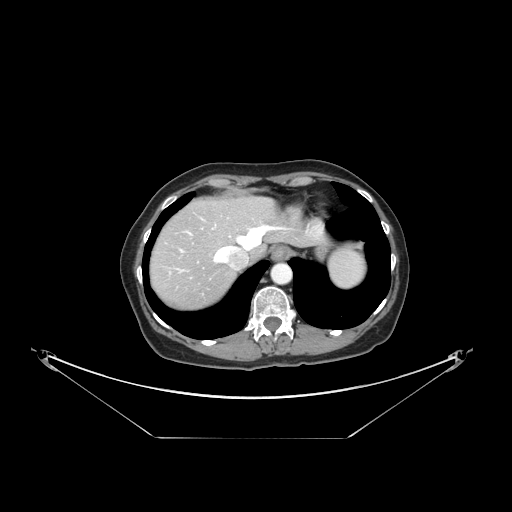
Contrast-enhanced abdominal CT, one axial slice; position 126 of 148 along the scan axis; reconstruction kernel STANDARD; 120 kVp; intravenous contrast given; soft-tissue window (W 400 / L 40 HU); 2.5 mm slice thickness; 512 × 512 image matrix, field of view 500 × 500 mm. Female patient, age 73 years. From the clinical record (not read from this slice): diagnosis: colorectal cancer liver metastases, imaged before liver resection; multiple liver metastases: no; largest metastasis: 1 cm; disease in both lobes: no.
Annotated regions visible in this slice (expert manual segmentation):
- hepatic veins: bounding box [x1, y1, x2, y2] px = [188, 225, 289, 263]
- liver: [151, 198, 315, 309]
- planned liver remnant (the part of the liver to remain after resection): [179, 198, 311, 254]